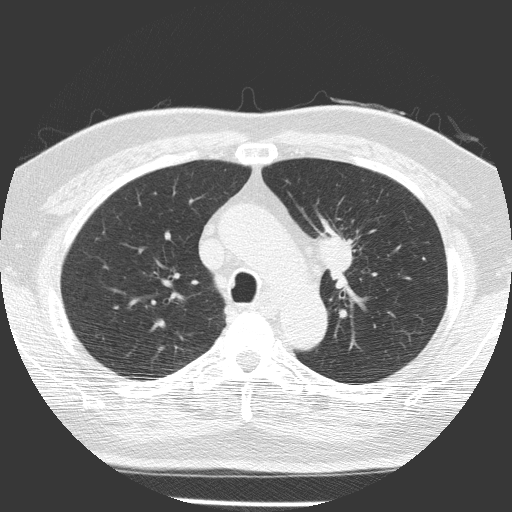
Low-dose screening chest CT, axial slice; first (baseline) screen; lung window (W 1500 / L -600 HU); lung (sharp) reconstruction kernel (FC51); 120 kVp; slice 48 of 156 in the series. Male participant, aged 70 years at enrolment. Current smoker at enrolment.
• Expert-annotated lung lesion, bounding box [x1, y1, x2, y2] px = [299, 224, 371, 299].
• The screening reader recorded 3 non-calcified nodules or masses ≥4 mm on this exam (left upper lobe, left lower lobe, left upper lobe); which of them this box marks is not recorded.
• Later outcome: lung cancer diagnosed 58 days after this screen — squamous cell carcinoma, NOS, left upper lobe, poorly differentiated (G3), stage IB (AJCC 6th edition), 47 mm at pathology.